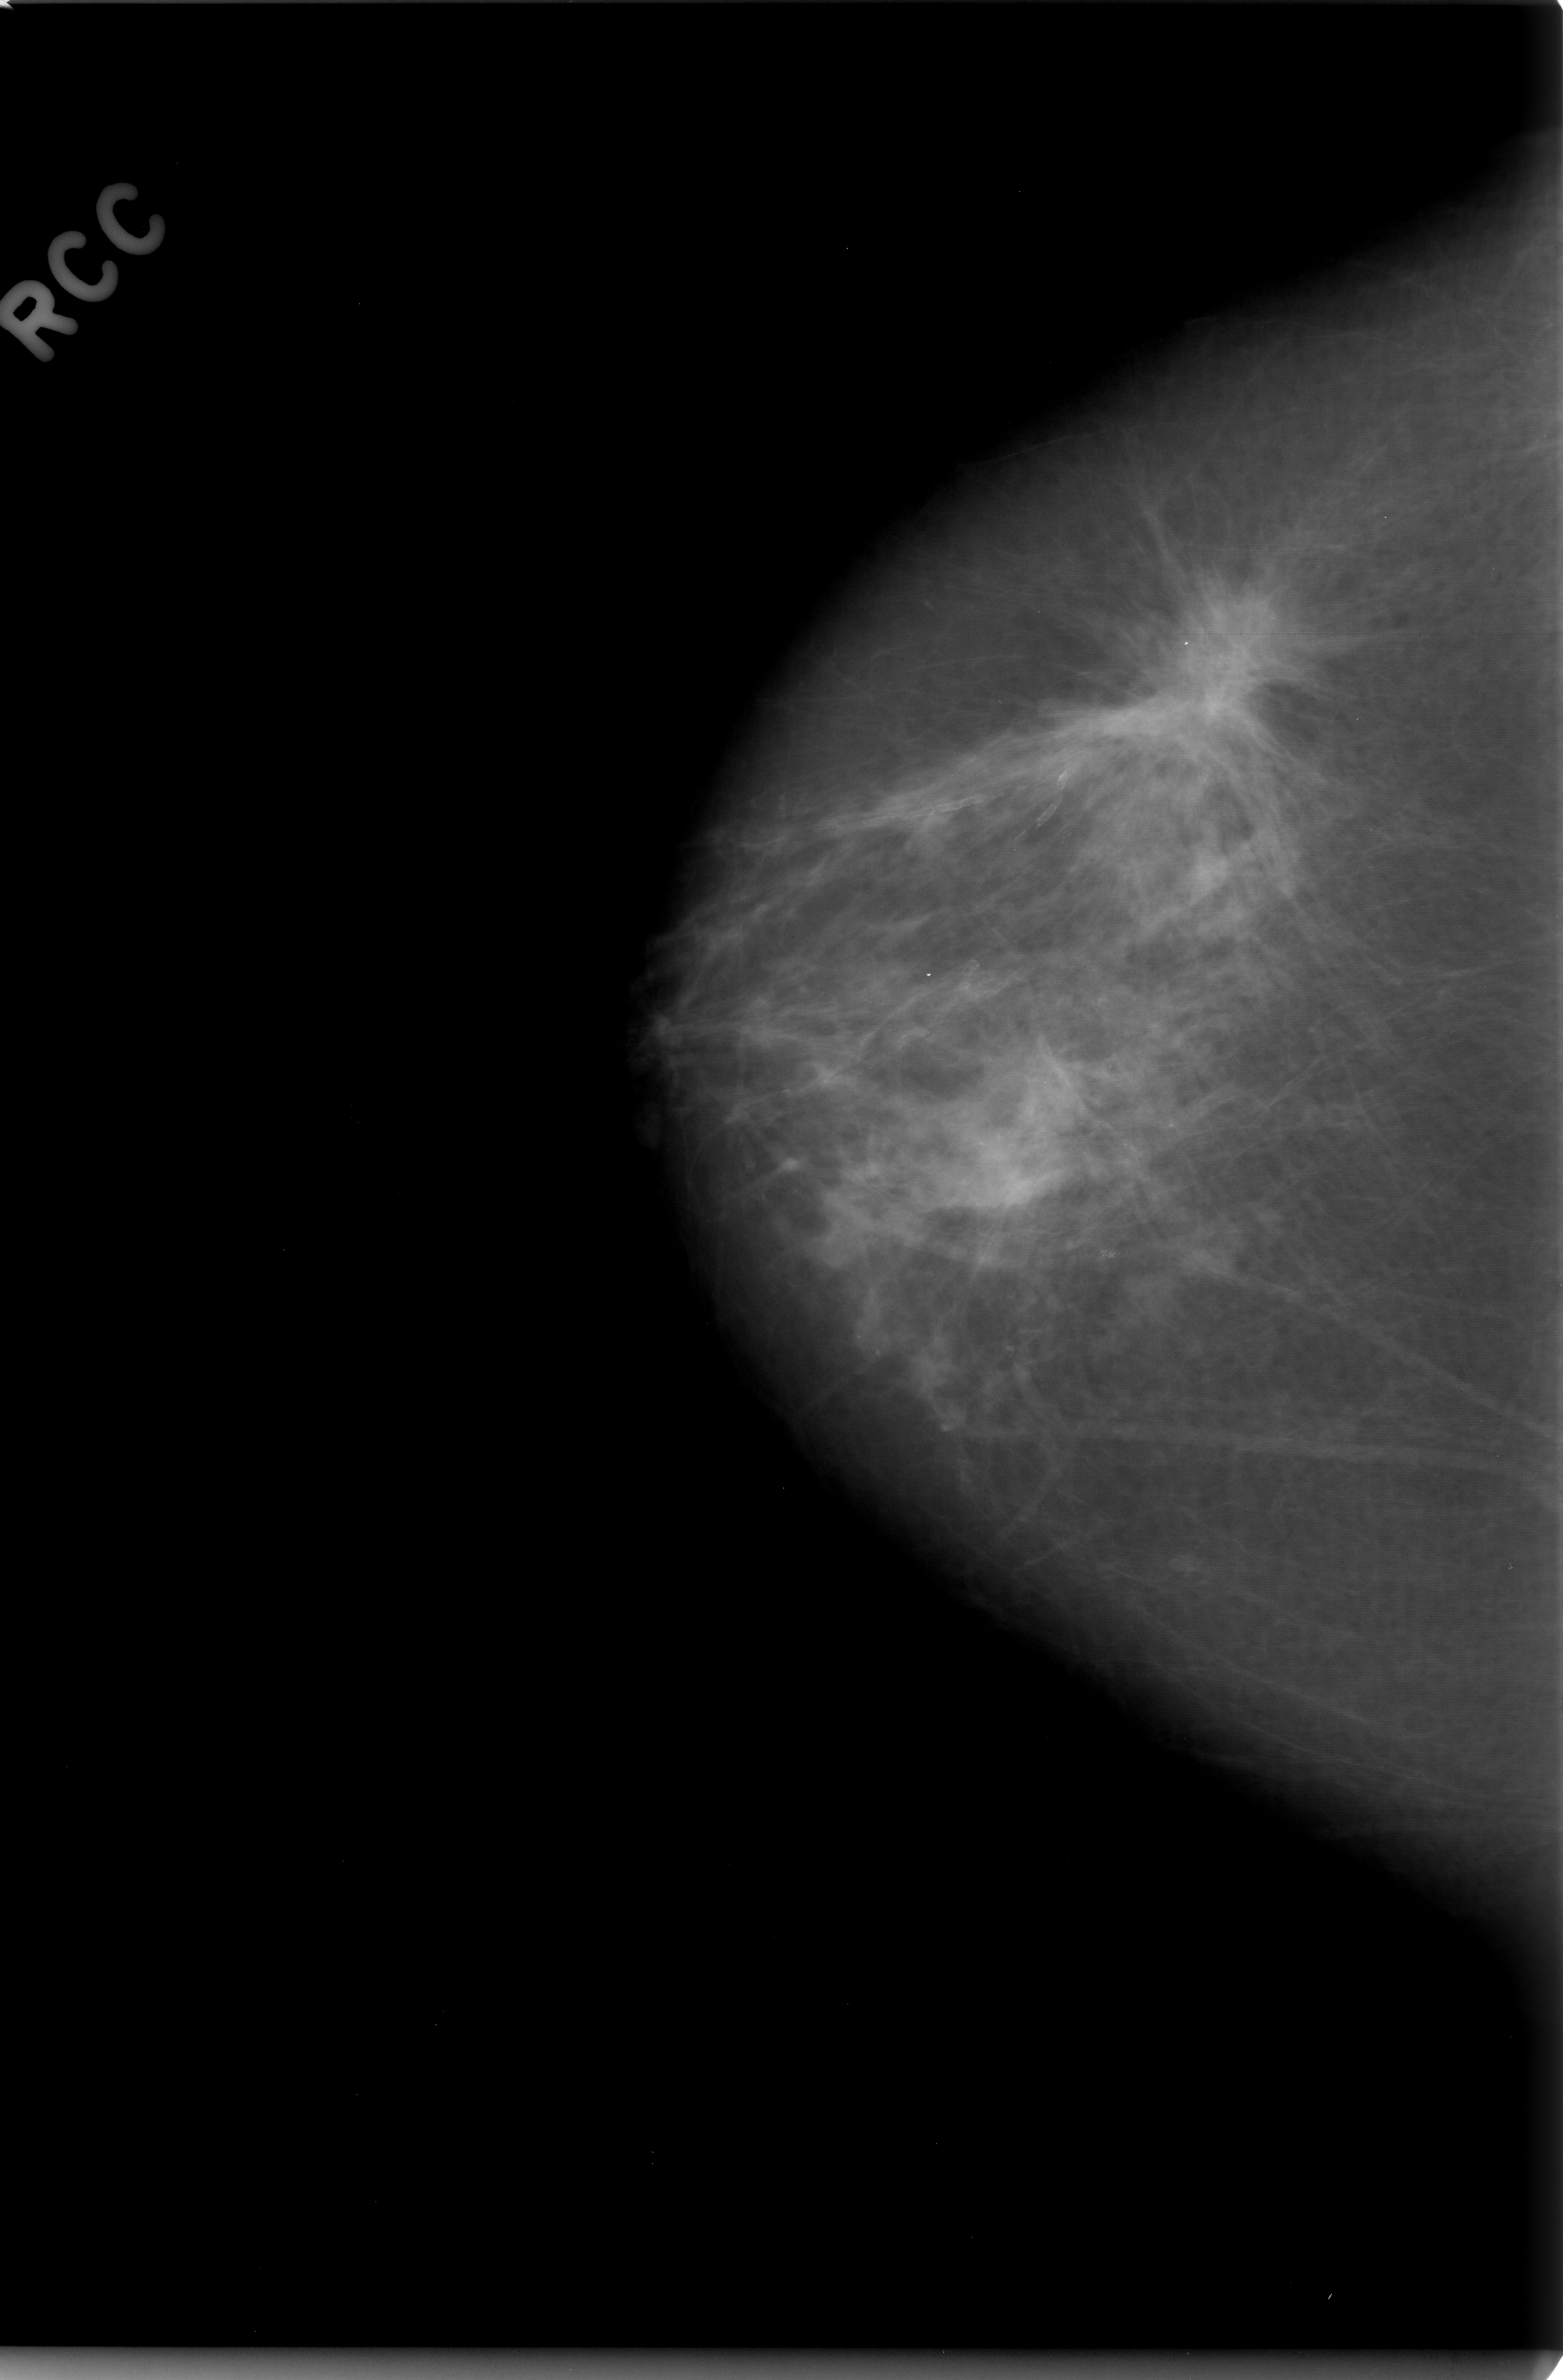
Mammogram (digitized film), right breast, CC view, BI-RADS breast density category 2 (scale 1–4).
- Finding: mass, shape architectural distortion, margins spiculated; BI-RADS assessment category 2; pathology result (as recorded, not read from the image): benign.